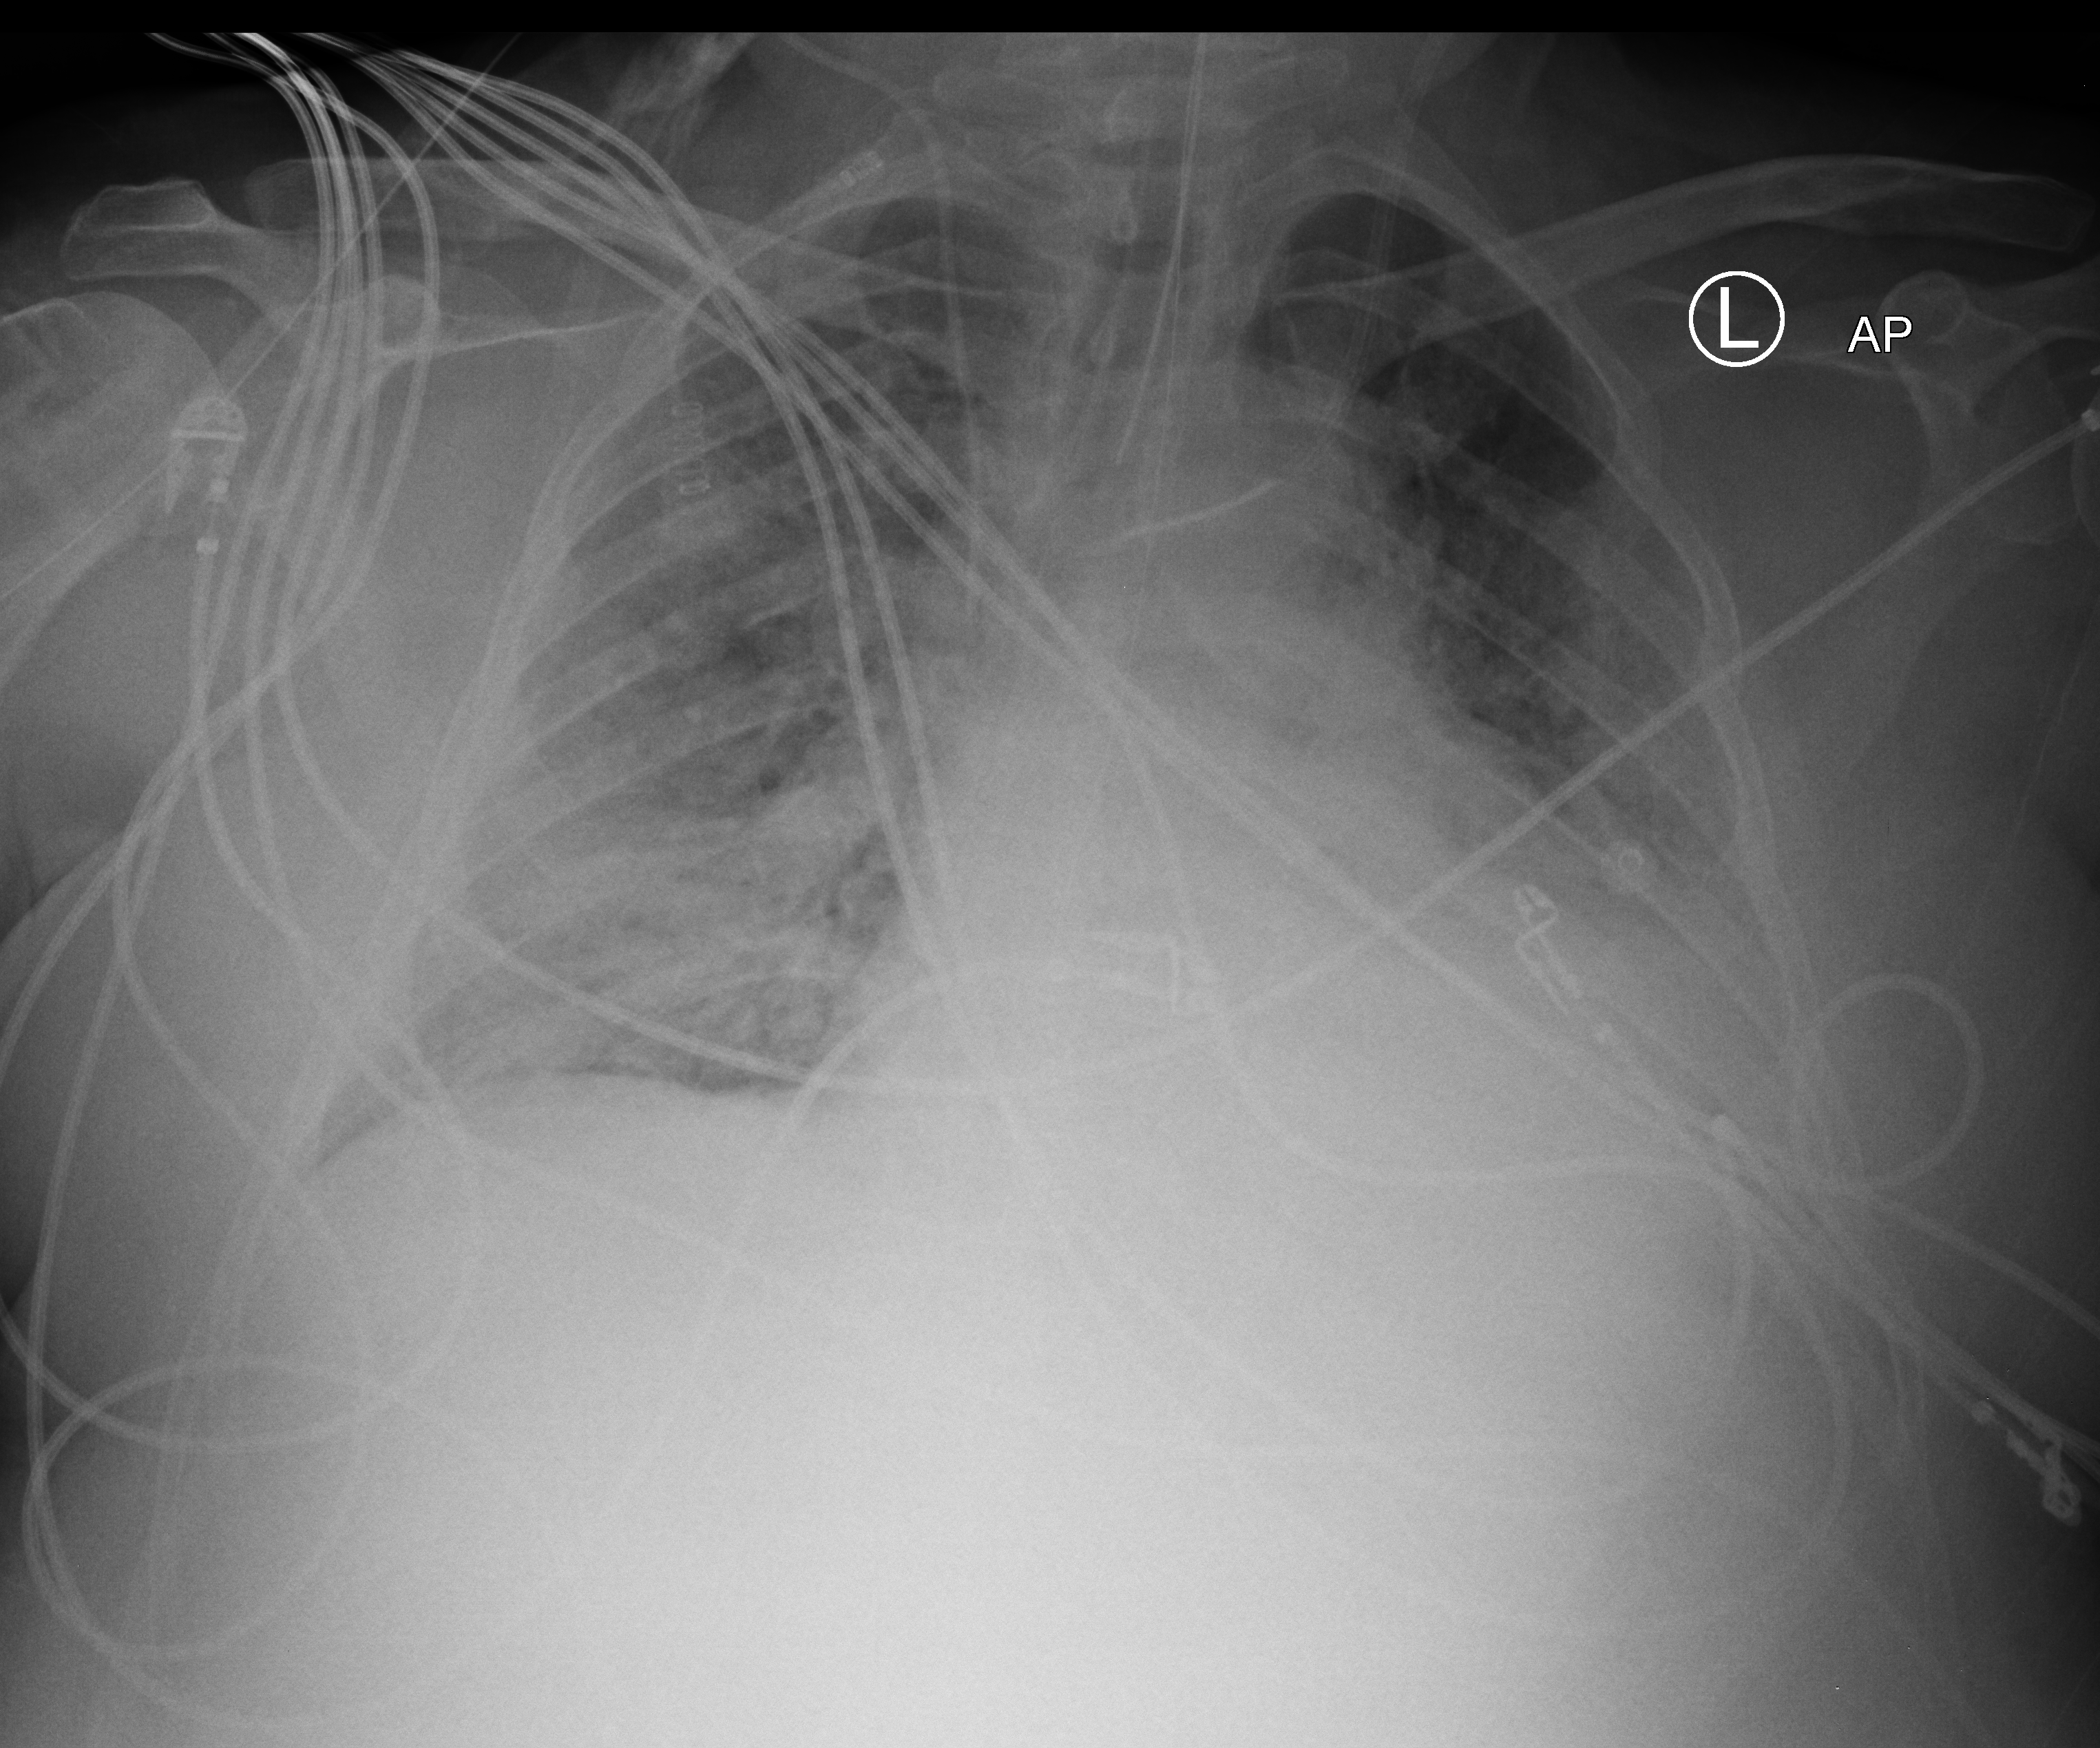
Portable chest radiograph; anteroposterior (AP) projection. Male patient hospitalised with COVID-19, age 18–59 years.
From the hospital-stay record, not from the radiograph (when in the stay this image was taken is not recorded): smoking status (admission record): never; mechanically ventilated during this hospital stay: yes.